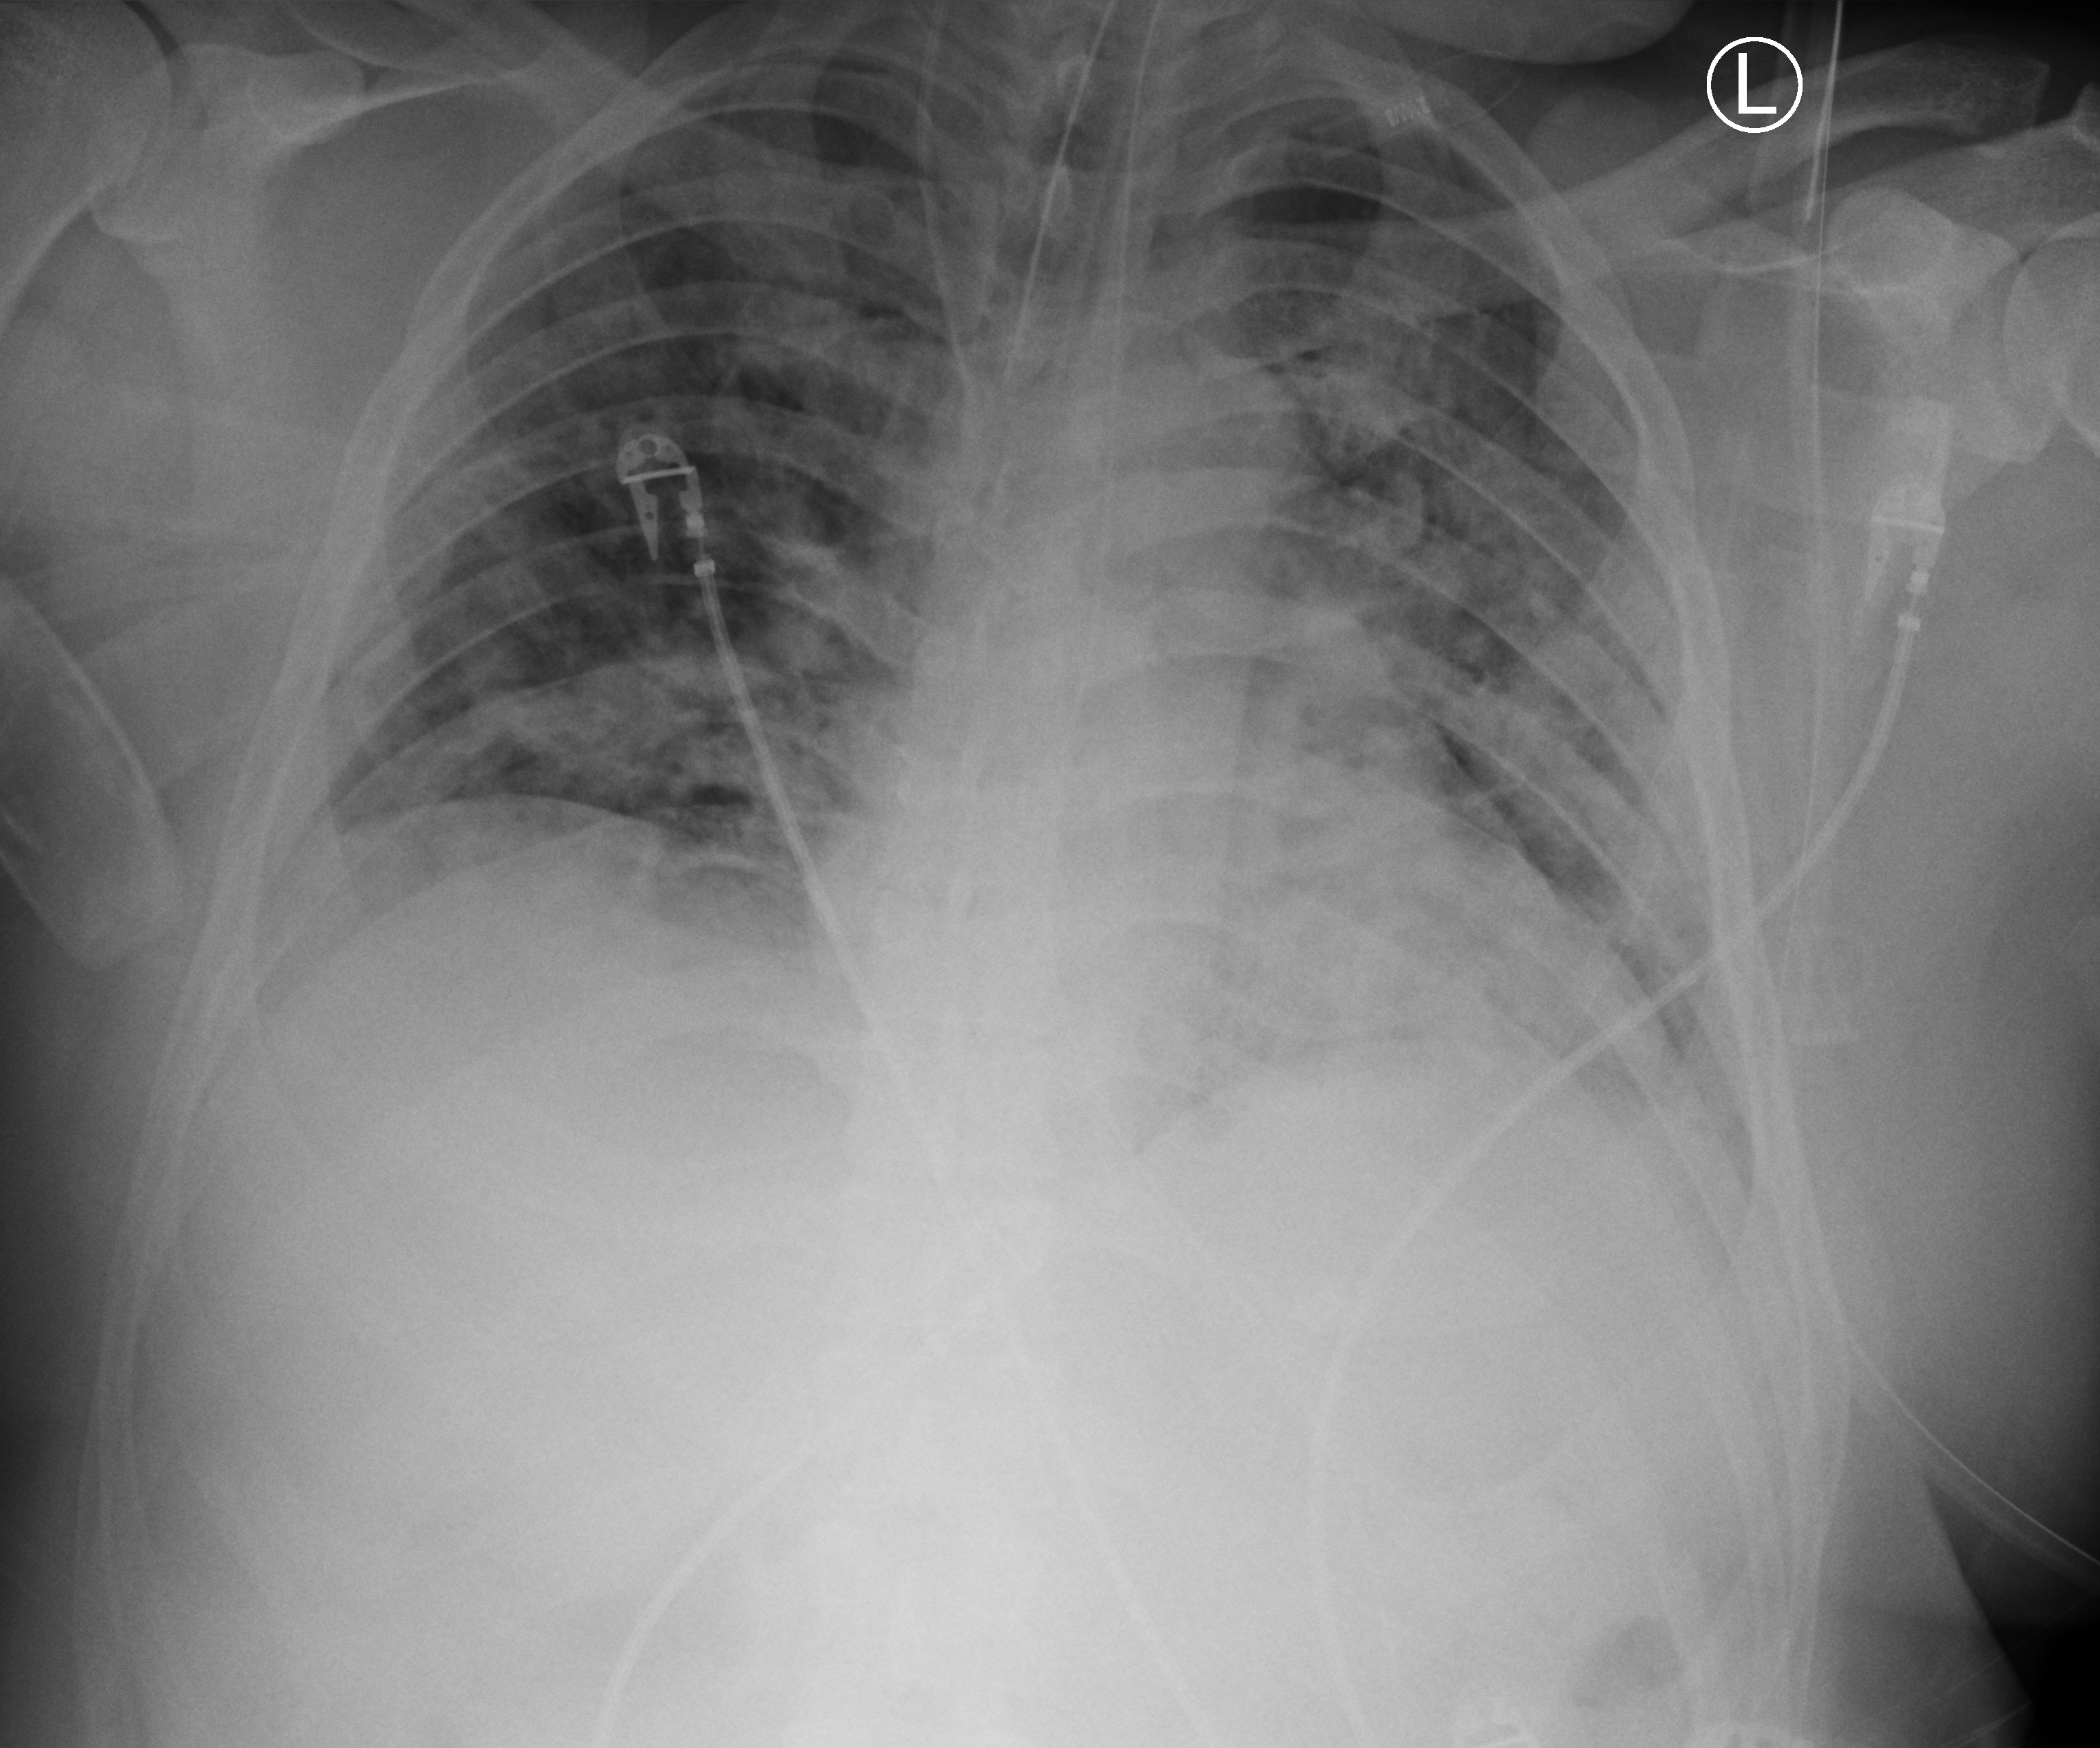
Bedside chest radiograph (computed radiography). Male patient hospitalised with COVID-19, age 18–59 years.
Admission-level facts for this patient (not findings on this image; timing relative to this image not recorded): admitted to intensive care during this hospital stay: yes.